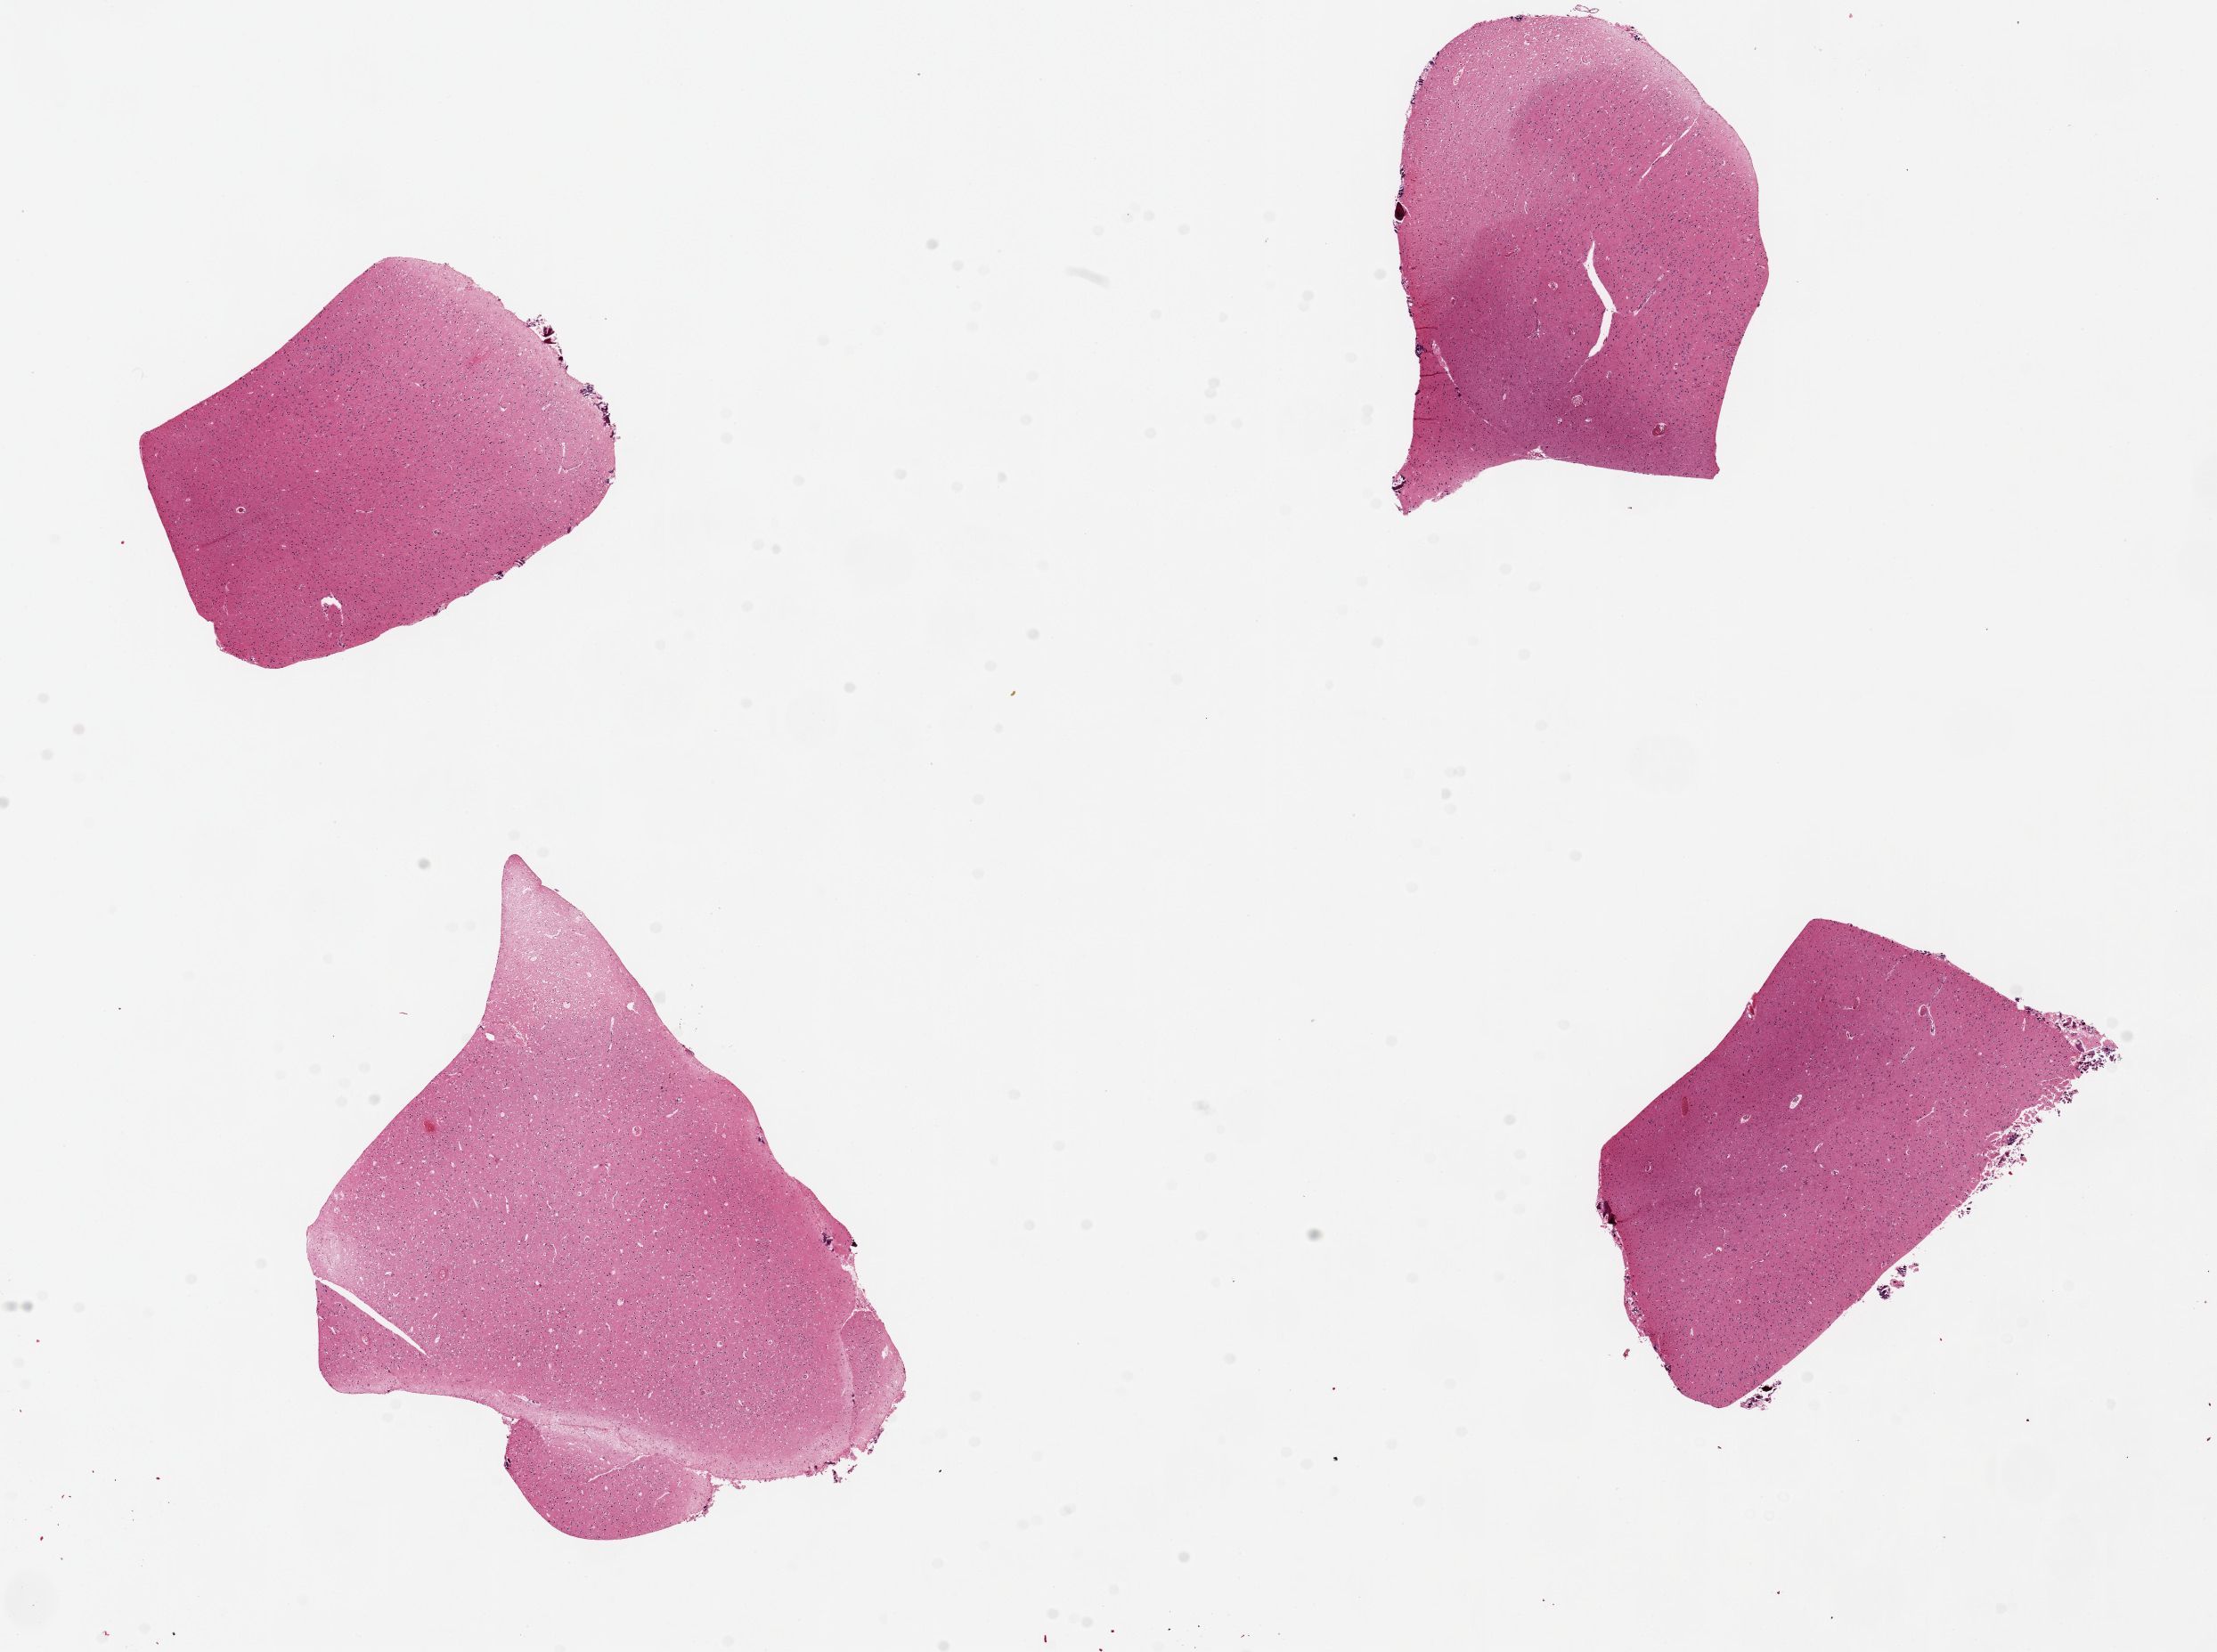
Hematoxylin and eosin (H&E) whole-slide image — whole scanned area (about 19.7 x 14.7 mm) shown as a low-resolution overview. PAXgene-fixed paraffin-embedded (PFPE) section. Sampled site (target tissue): cerebral cortex. Tissue donor sample. Donor sex: male.
Review note (as recorded): 4 pieces ~~4x3mm.